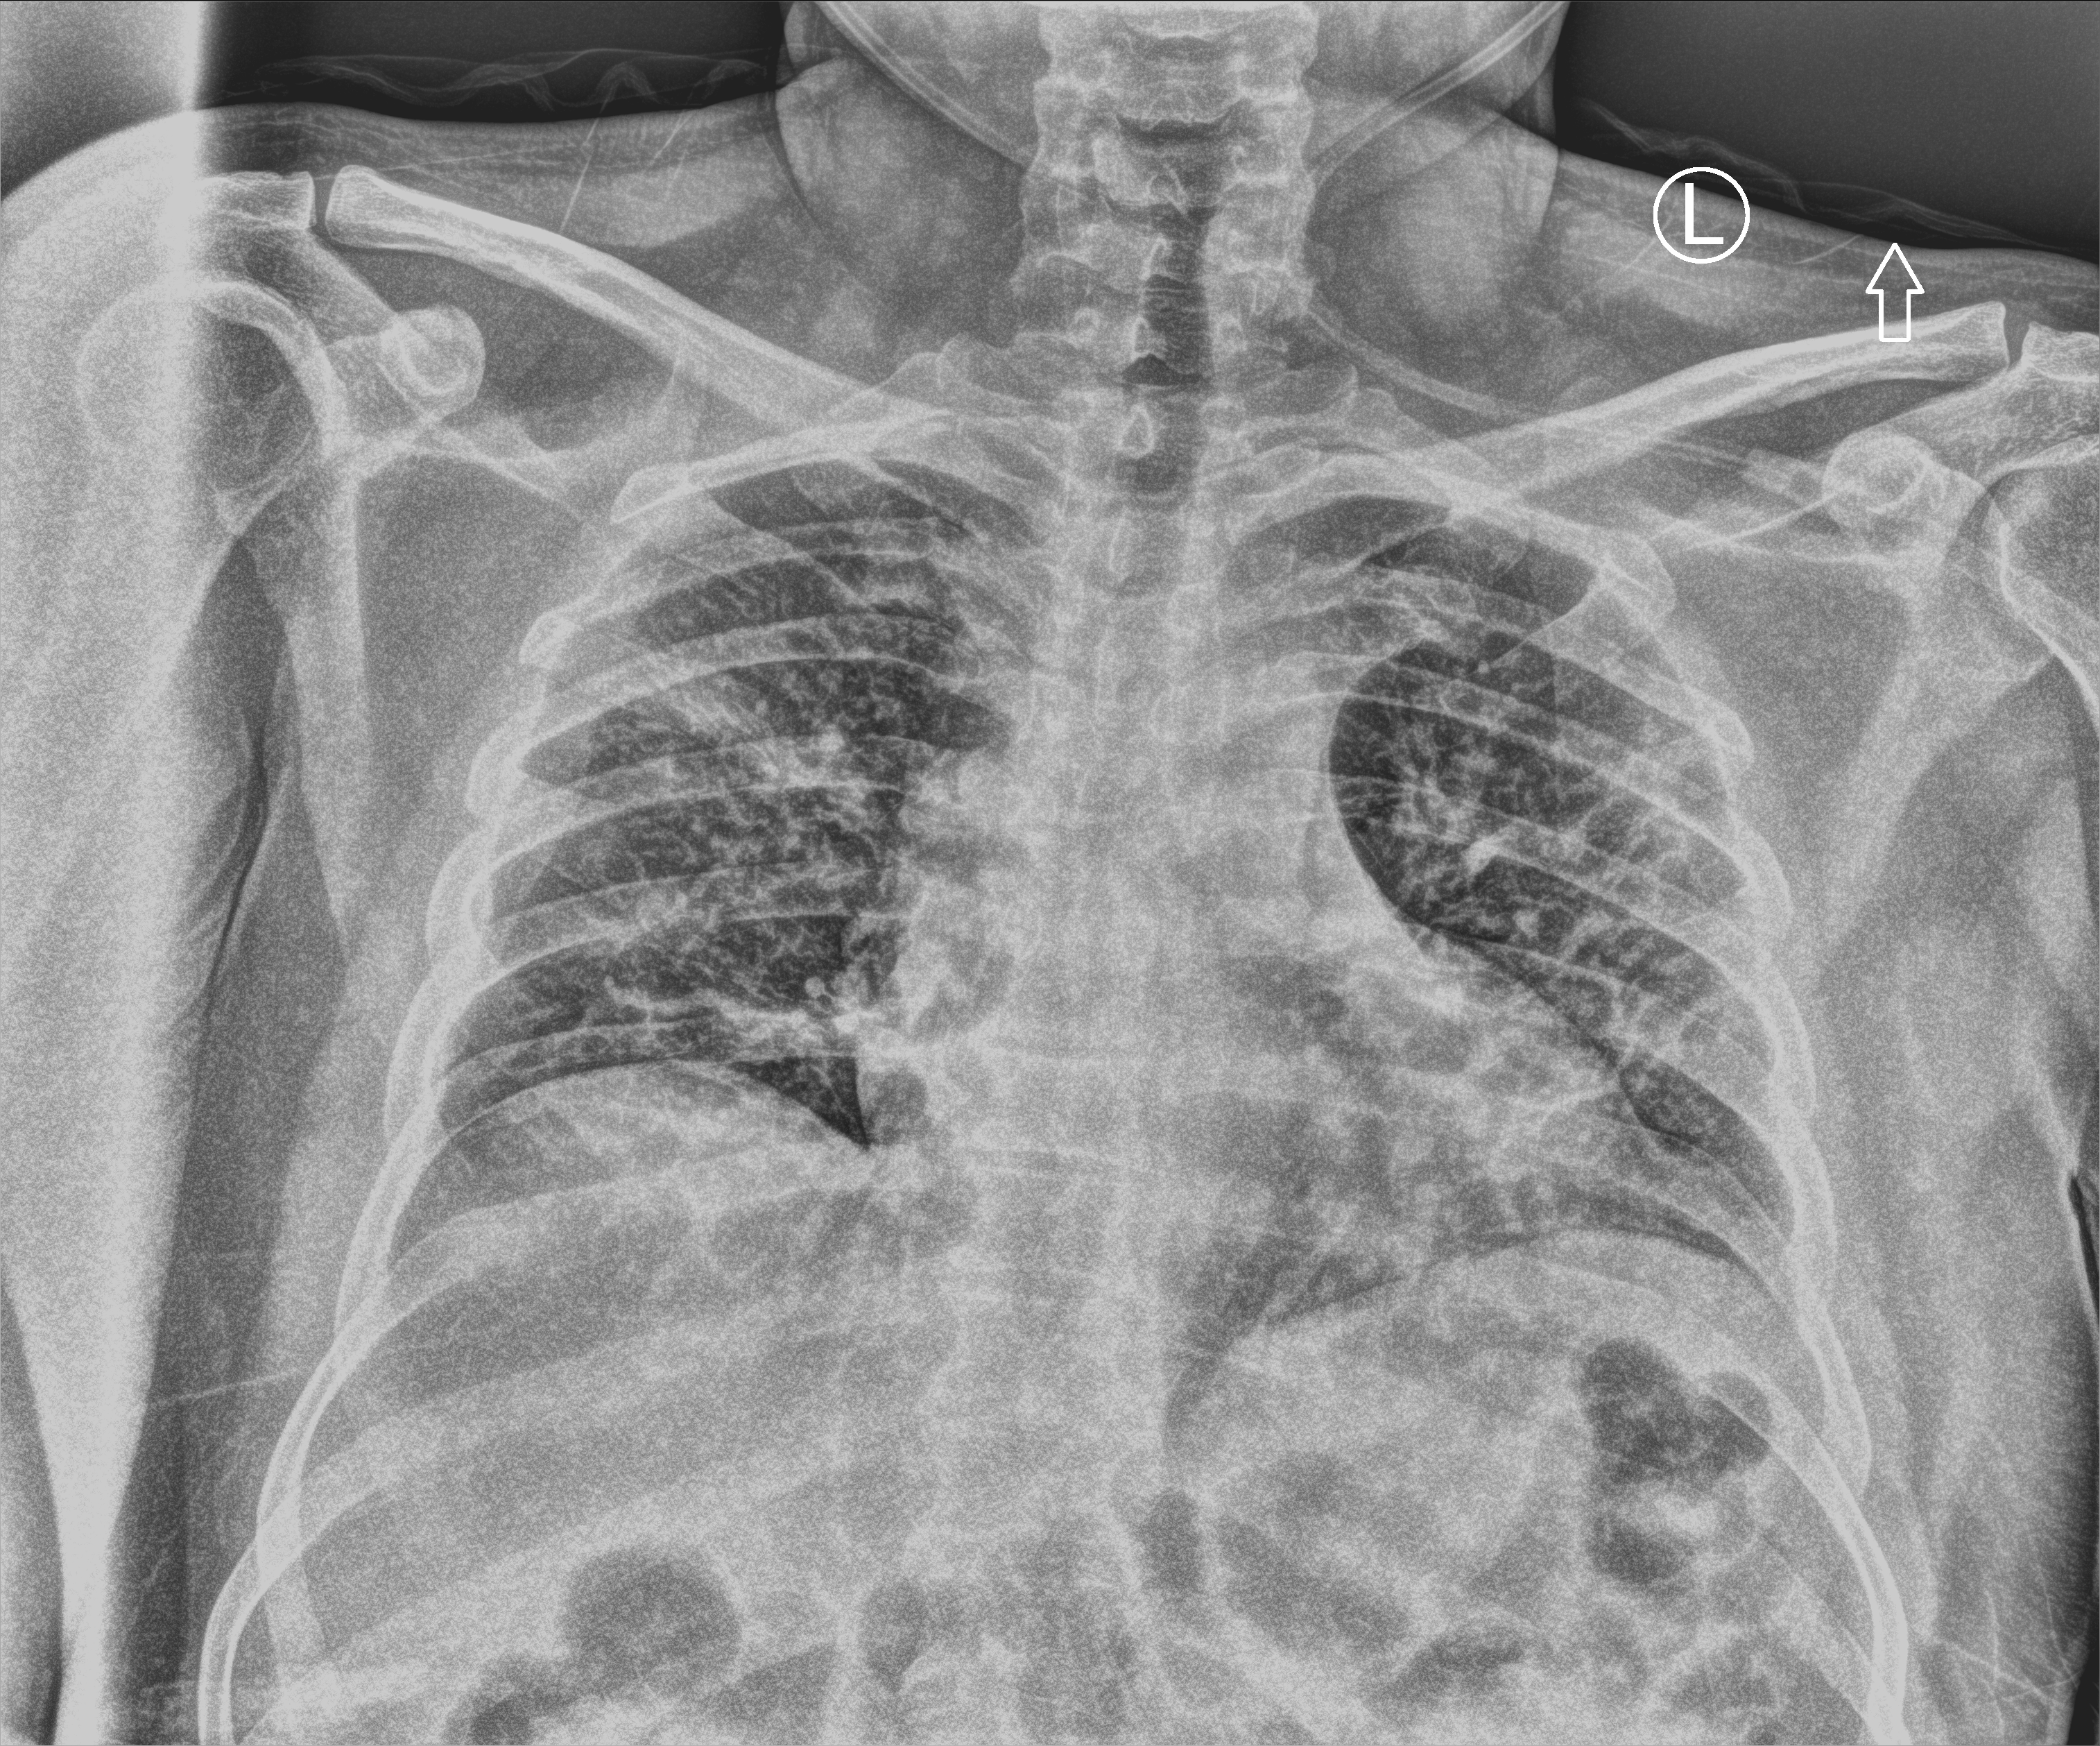
Chest X-ray (portable), anteroposterior (AP) projection. Patient hospitalised with COVID-19; male, aged 18–59 years.
Admission-level facts for this patient (not findings on this image; timing relative to this image not recorded):
- length of hospital stay: 4 days